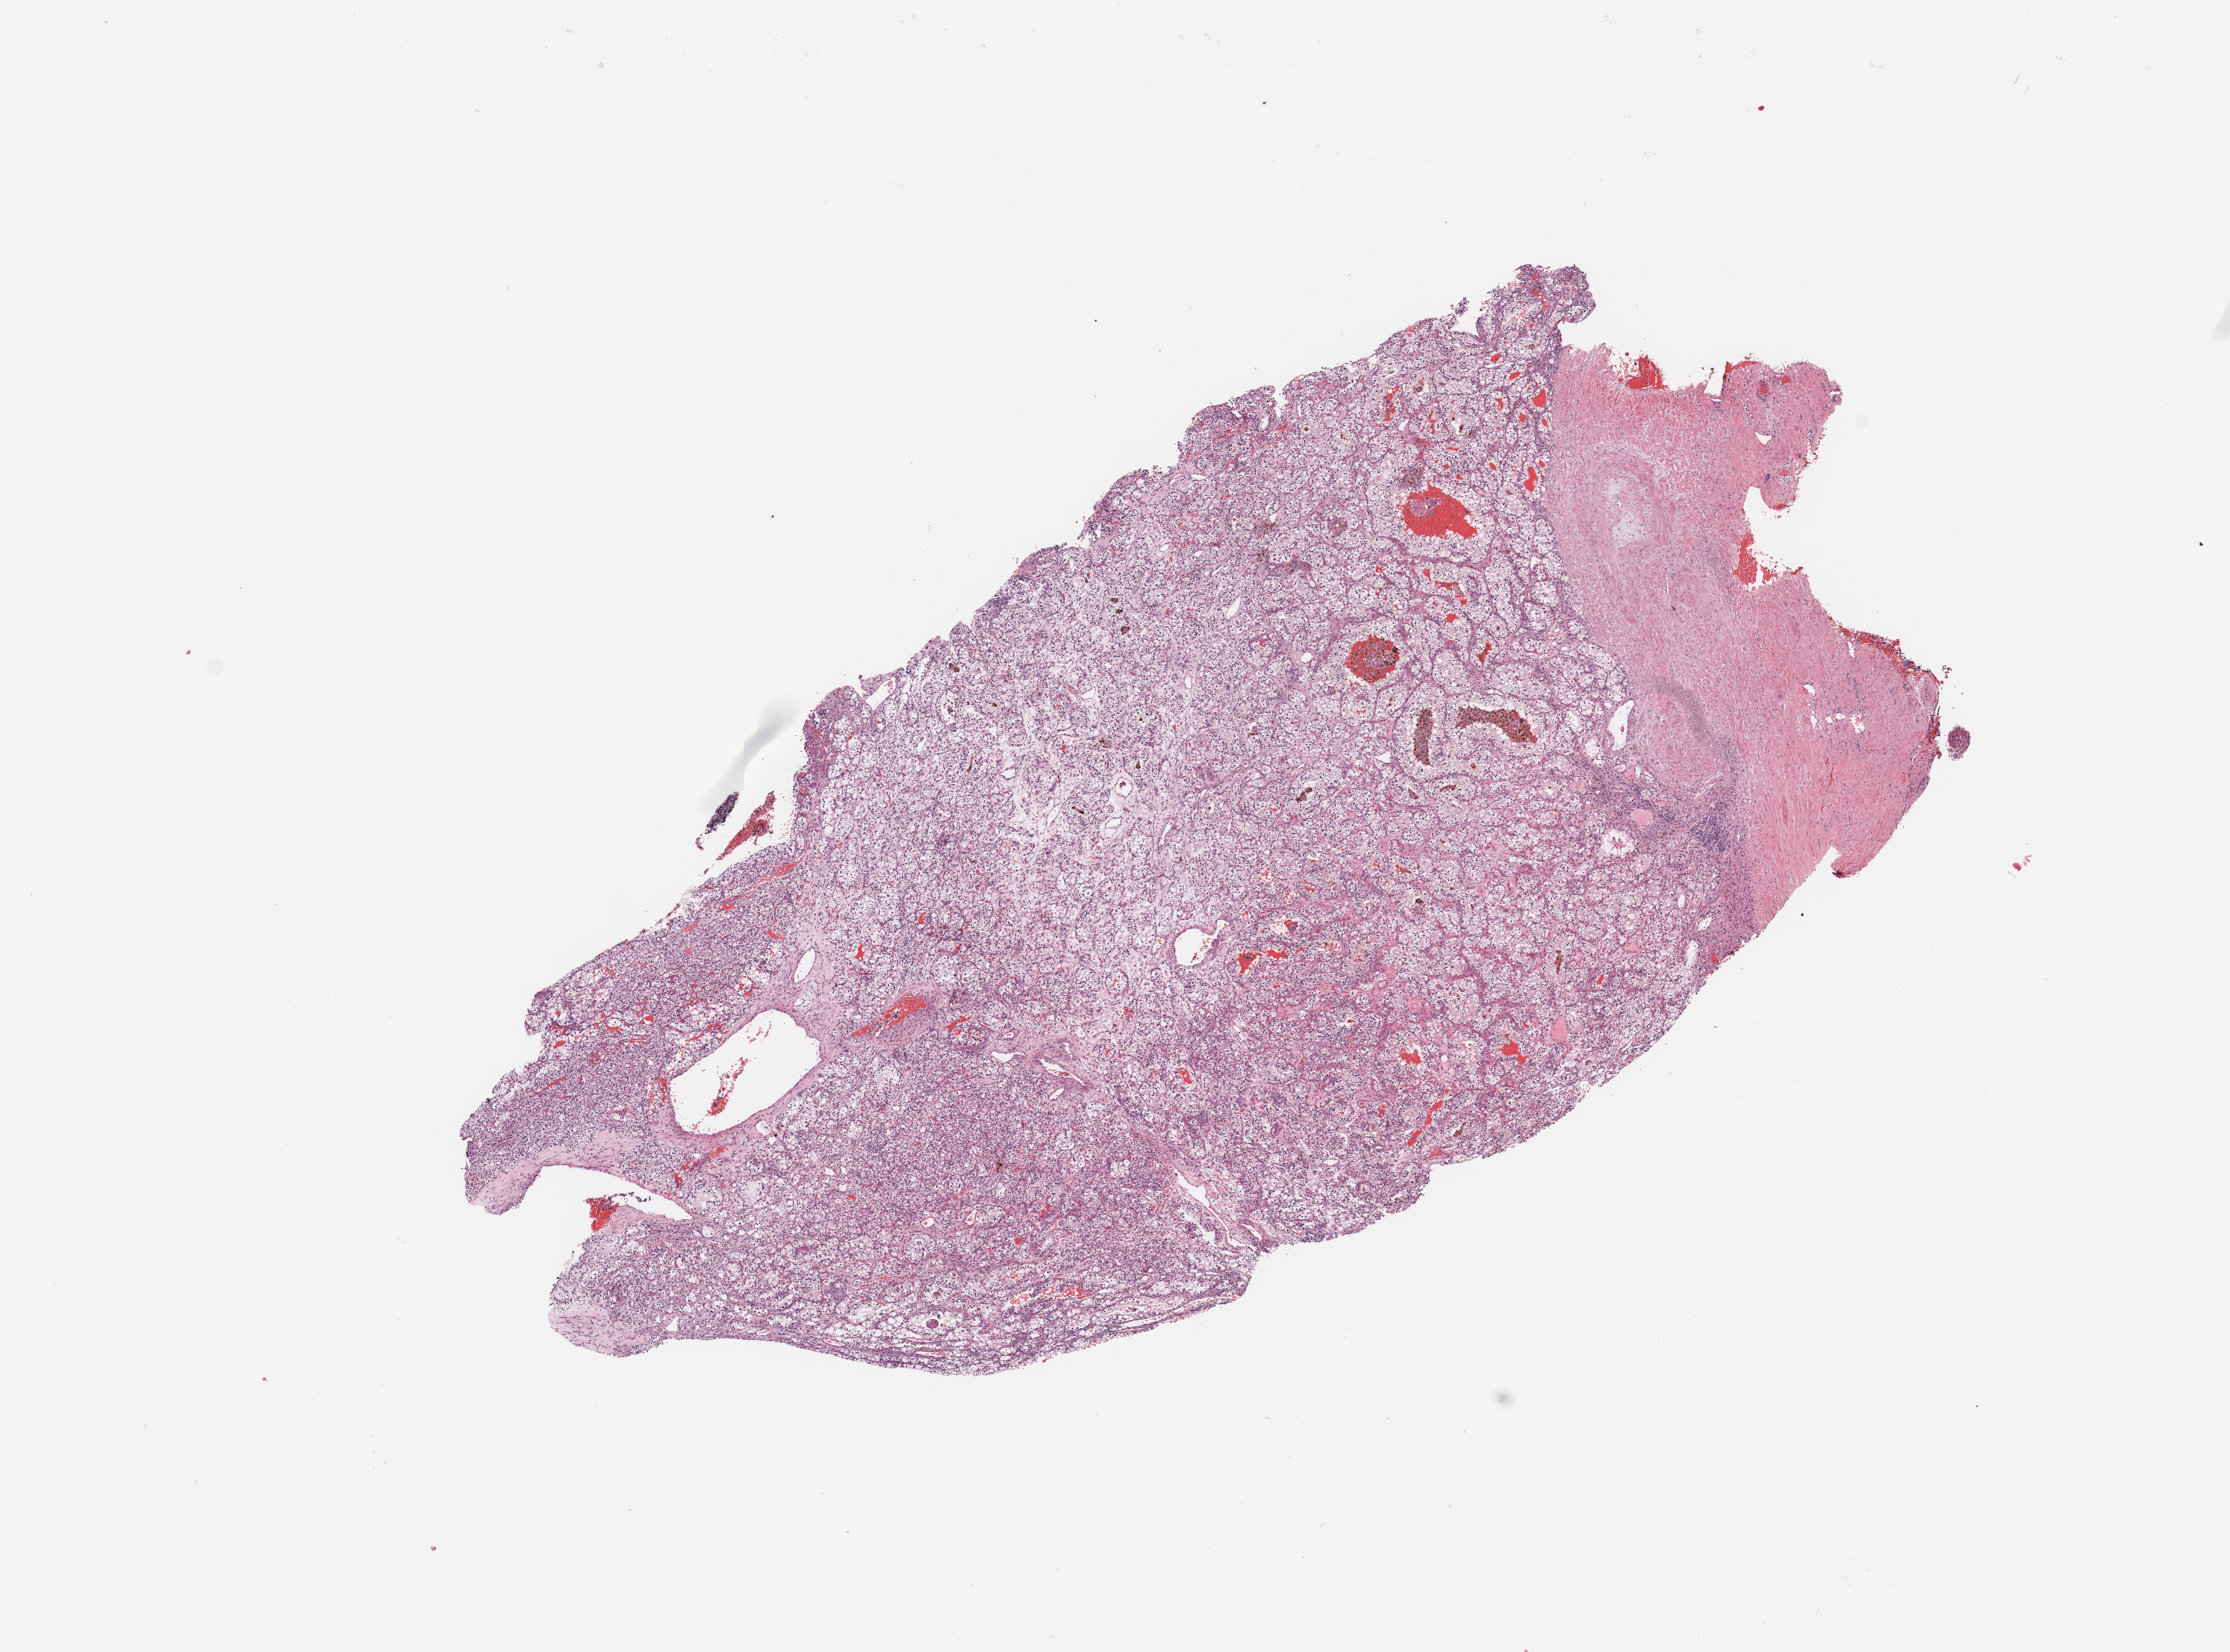
Whole-slide histology image, H&E, a low-resolution overview of the entire scanned area, about 11.8 x 8.8 mm (acquisition: 20x scan); tumour tissue sample, sampled site: kidney. Patient: male, age 41 years. Histologic grade: G2 (moderately differentiated). Composition of this section per pathologist review: tumour nuclei 90%, necrosis 5%.
Primary tumour site (as recorded): middle. AJCC pathologic stage: I. Histologic diagnosis: Renal cell carcinoma, NOS.